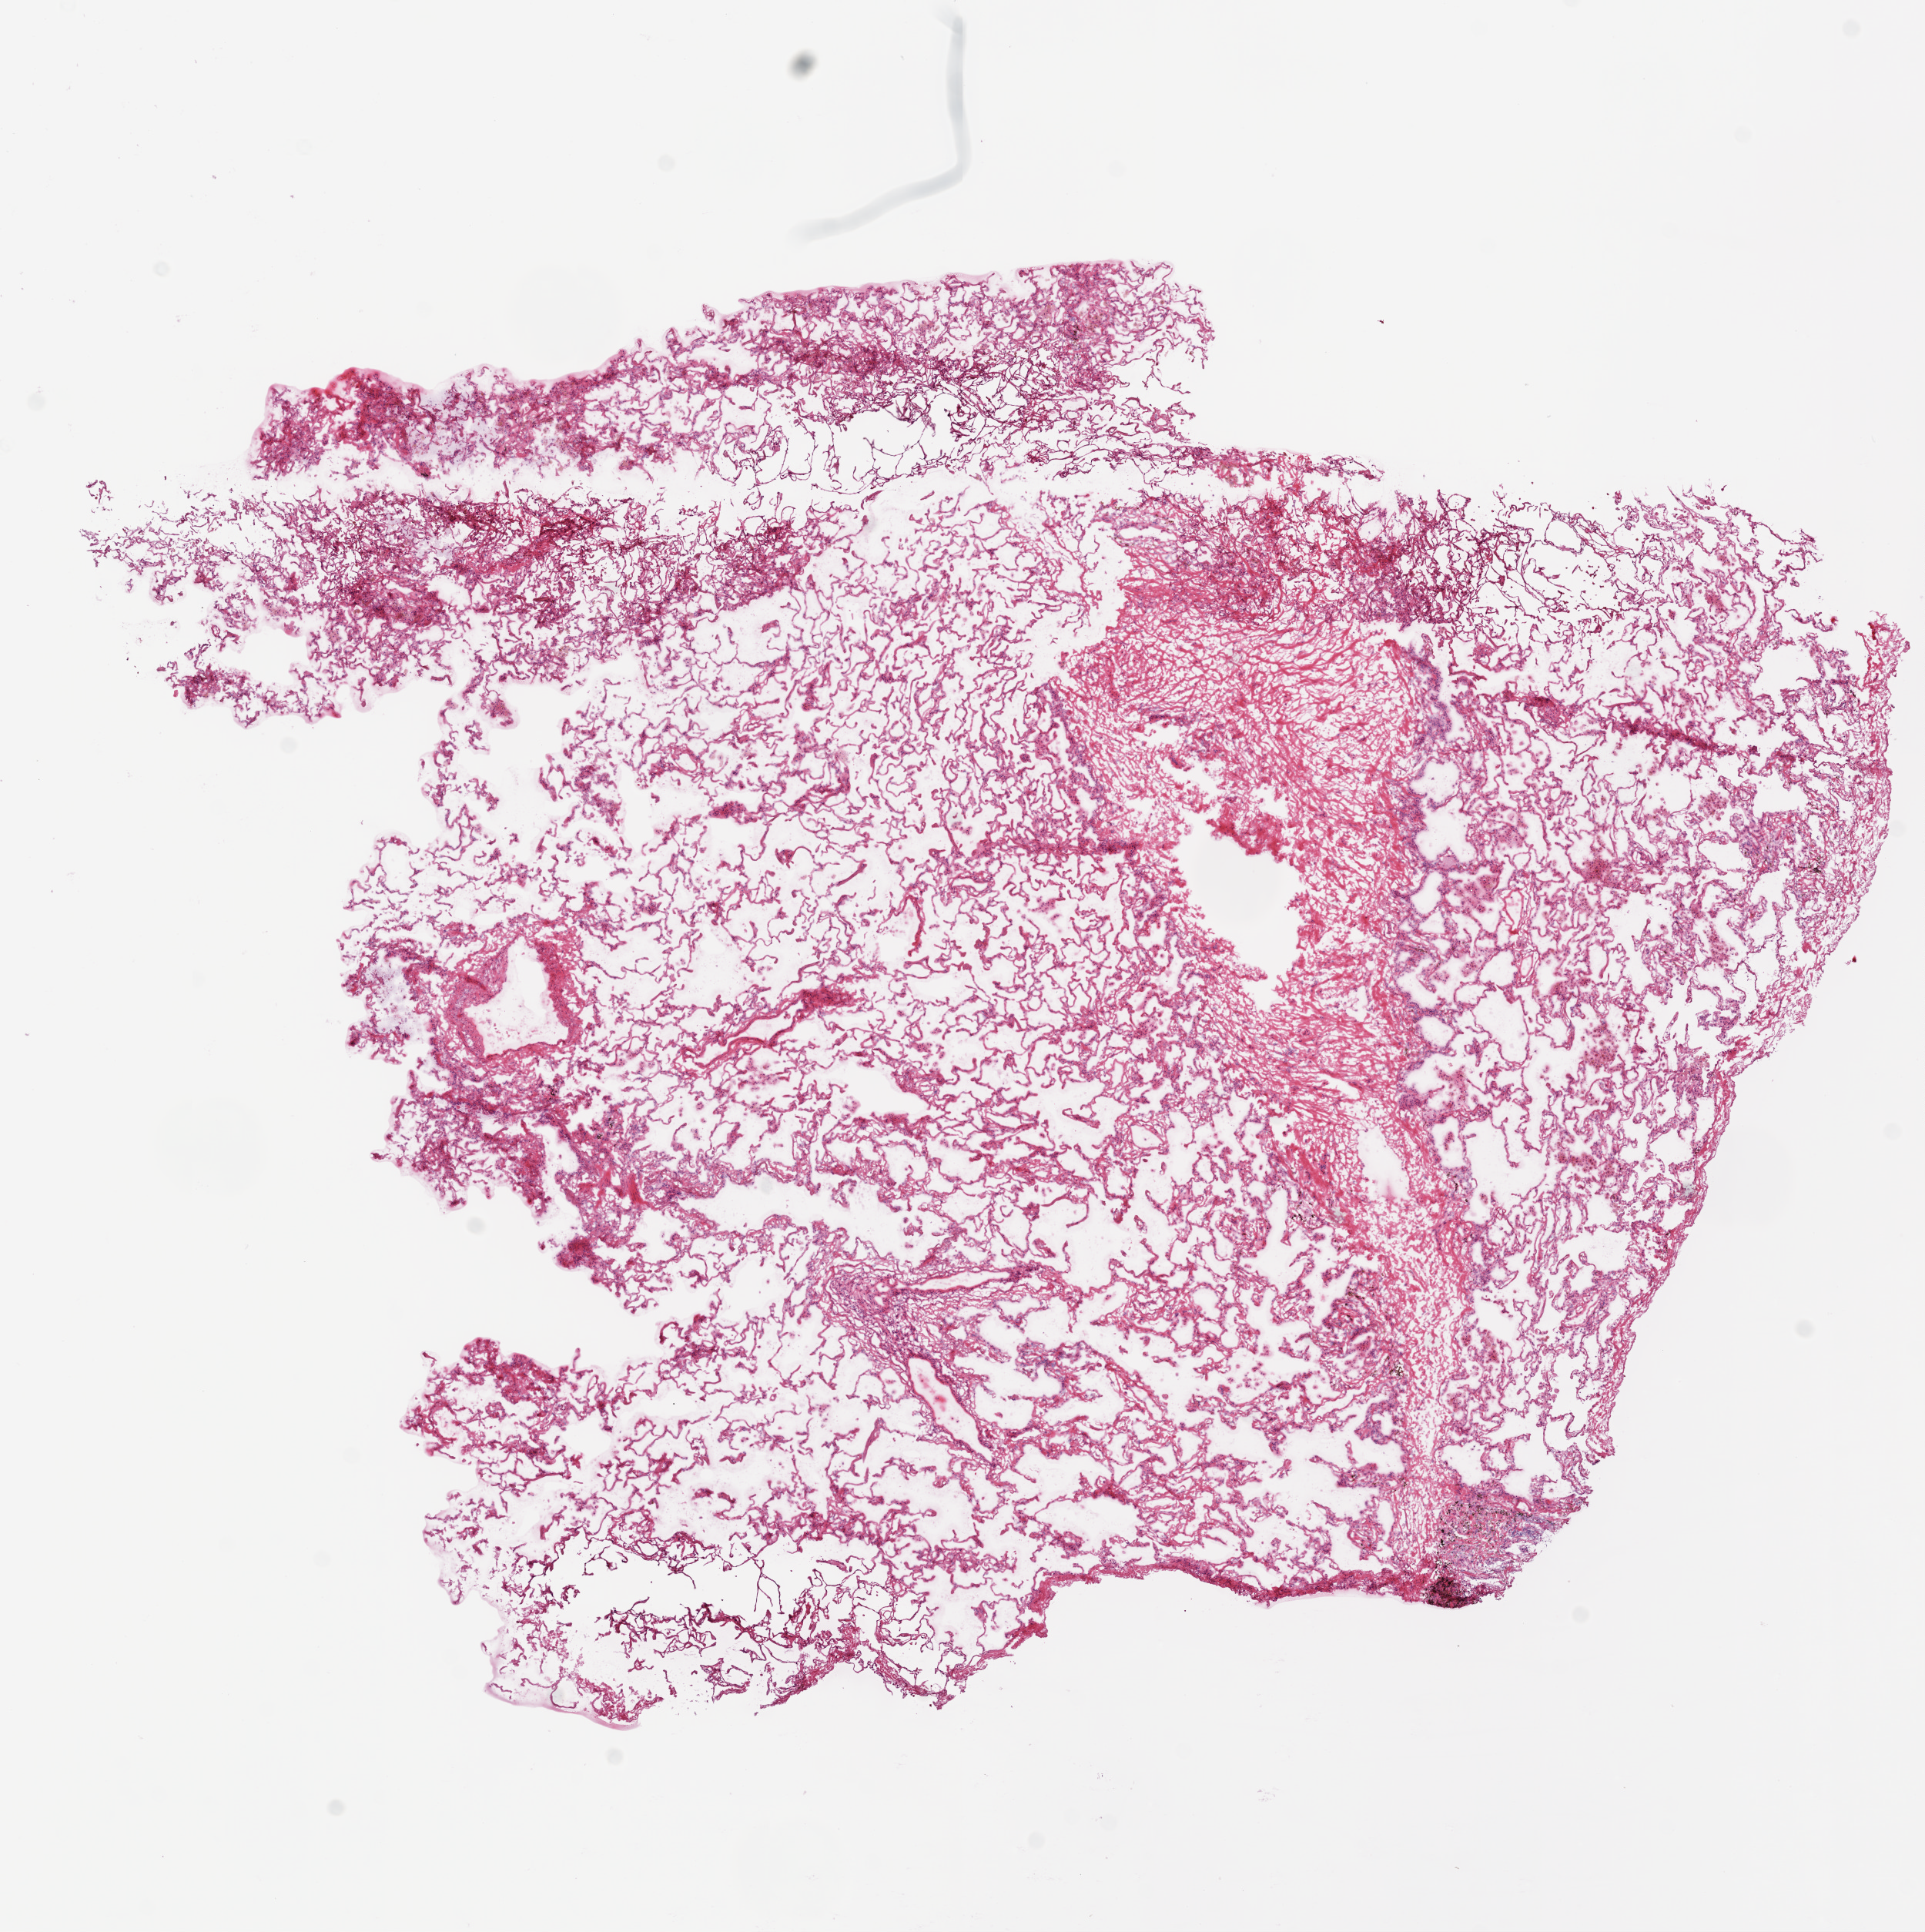
H&E whole-slide image — a low-resolution overview of the entire scanned area, about 10.0 x 10.1 mm (slide scanned at 20x); frozen section; lung, solid tissue normal (non-tumour tissue) sample. Female patient; age at initial diagnosis 58 years.
• this section: solid tissue normal sample (biorepository sample class)
• patient diagnosis: Squamous cell carcinoma, NOS (upper lobe, lung)